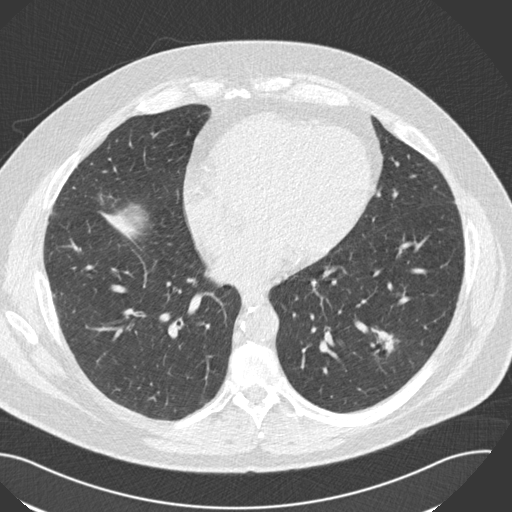
Low-dose screening chest CT, axial slice, third annual screen, lung window (W 1500 / L -600 HU), 512 × 512 image matrix, field of view 394 × 394 mm. Male participant, aged 57 years at enrolment. Current smoker at enrolment.
Expert reader's lesion annotation, box from (x=349, y=315) to (x=416, y=370) px. Screening reader's record for this exam (one nodule recorded; not confirmed to be the boxed lesion): non-calcified nodule or mass ≥4 mm, left lower lobe, 22 × 18 mm, poorly defined margins, soft tissue attenuation, pre-existing on the prior screen: yes; interval growth: yes. Official screen result: positive, other. Participant outcome: lung cancer diagnosed 124 days after this screen — squamous cell carcinoma, NOS, left lower lobe, moderately differentiated (G2), stage IA (AJCC 6th edition), 22 mm at pathology.